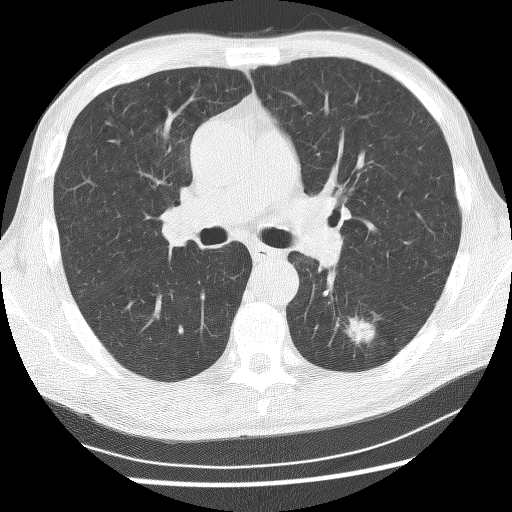
Low-dose screening chest CT, one axial slice. Slice 150 of 253 in the series (ordered by position). Lung window (W 1500 / L -600 HU). 512 × 512 image matrix, field of view 340 × 340 mm.
Annotated regions visible in this slice (expert manual segmentation):
- lesion 1 (tumor, lower lobe of left lung): box from (x=346, y=317) to (x=375, y=345) px